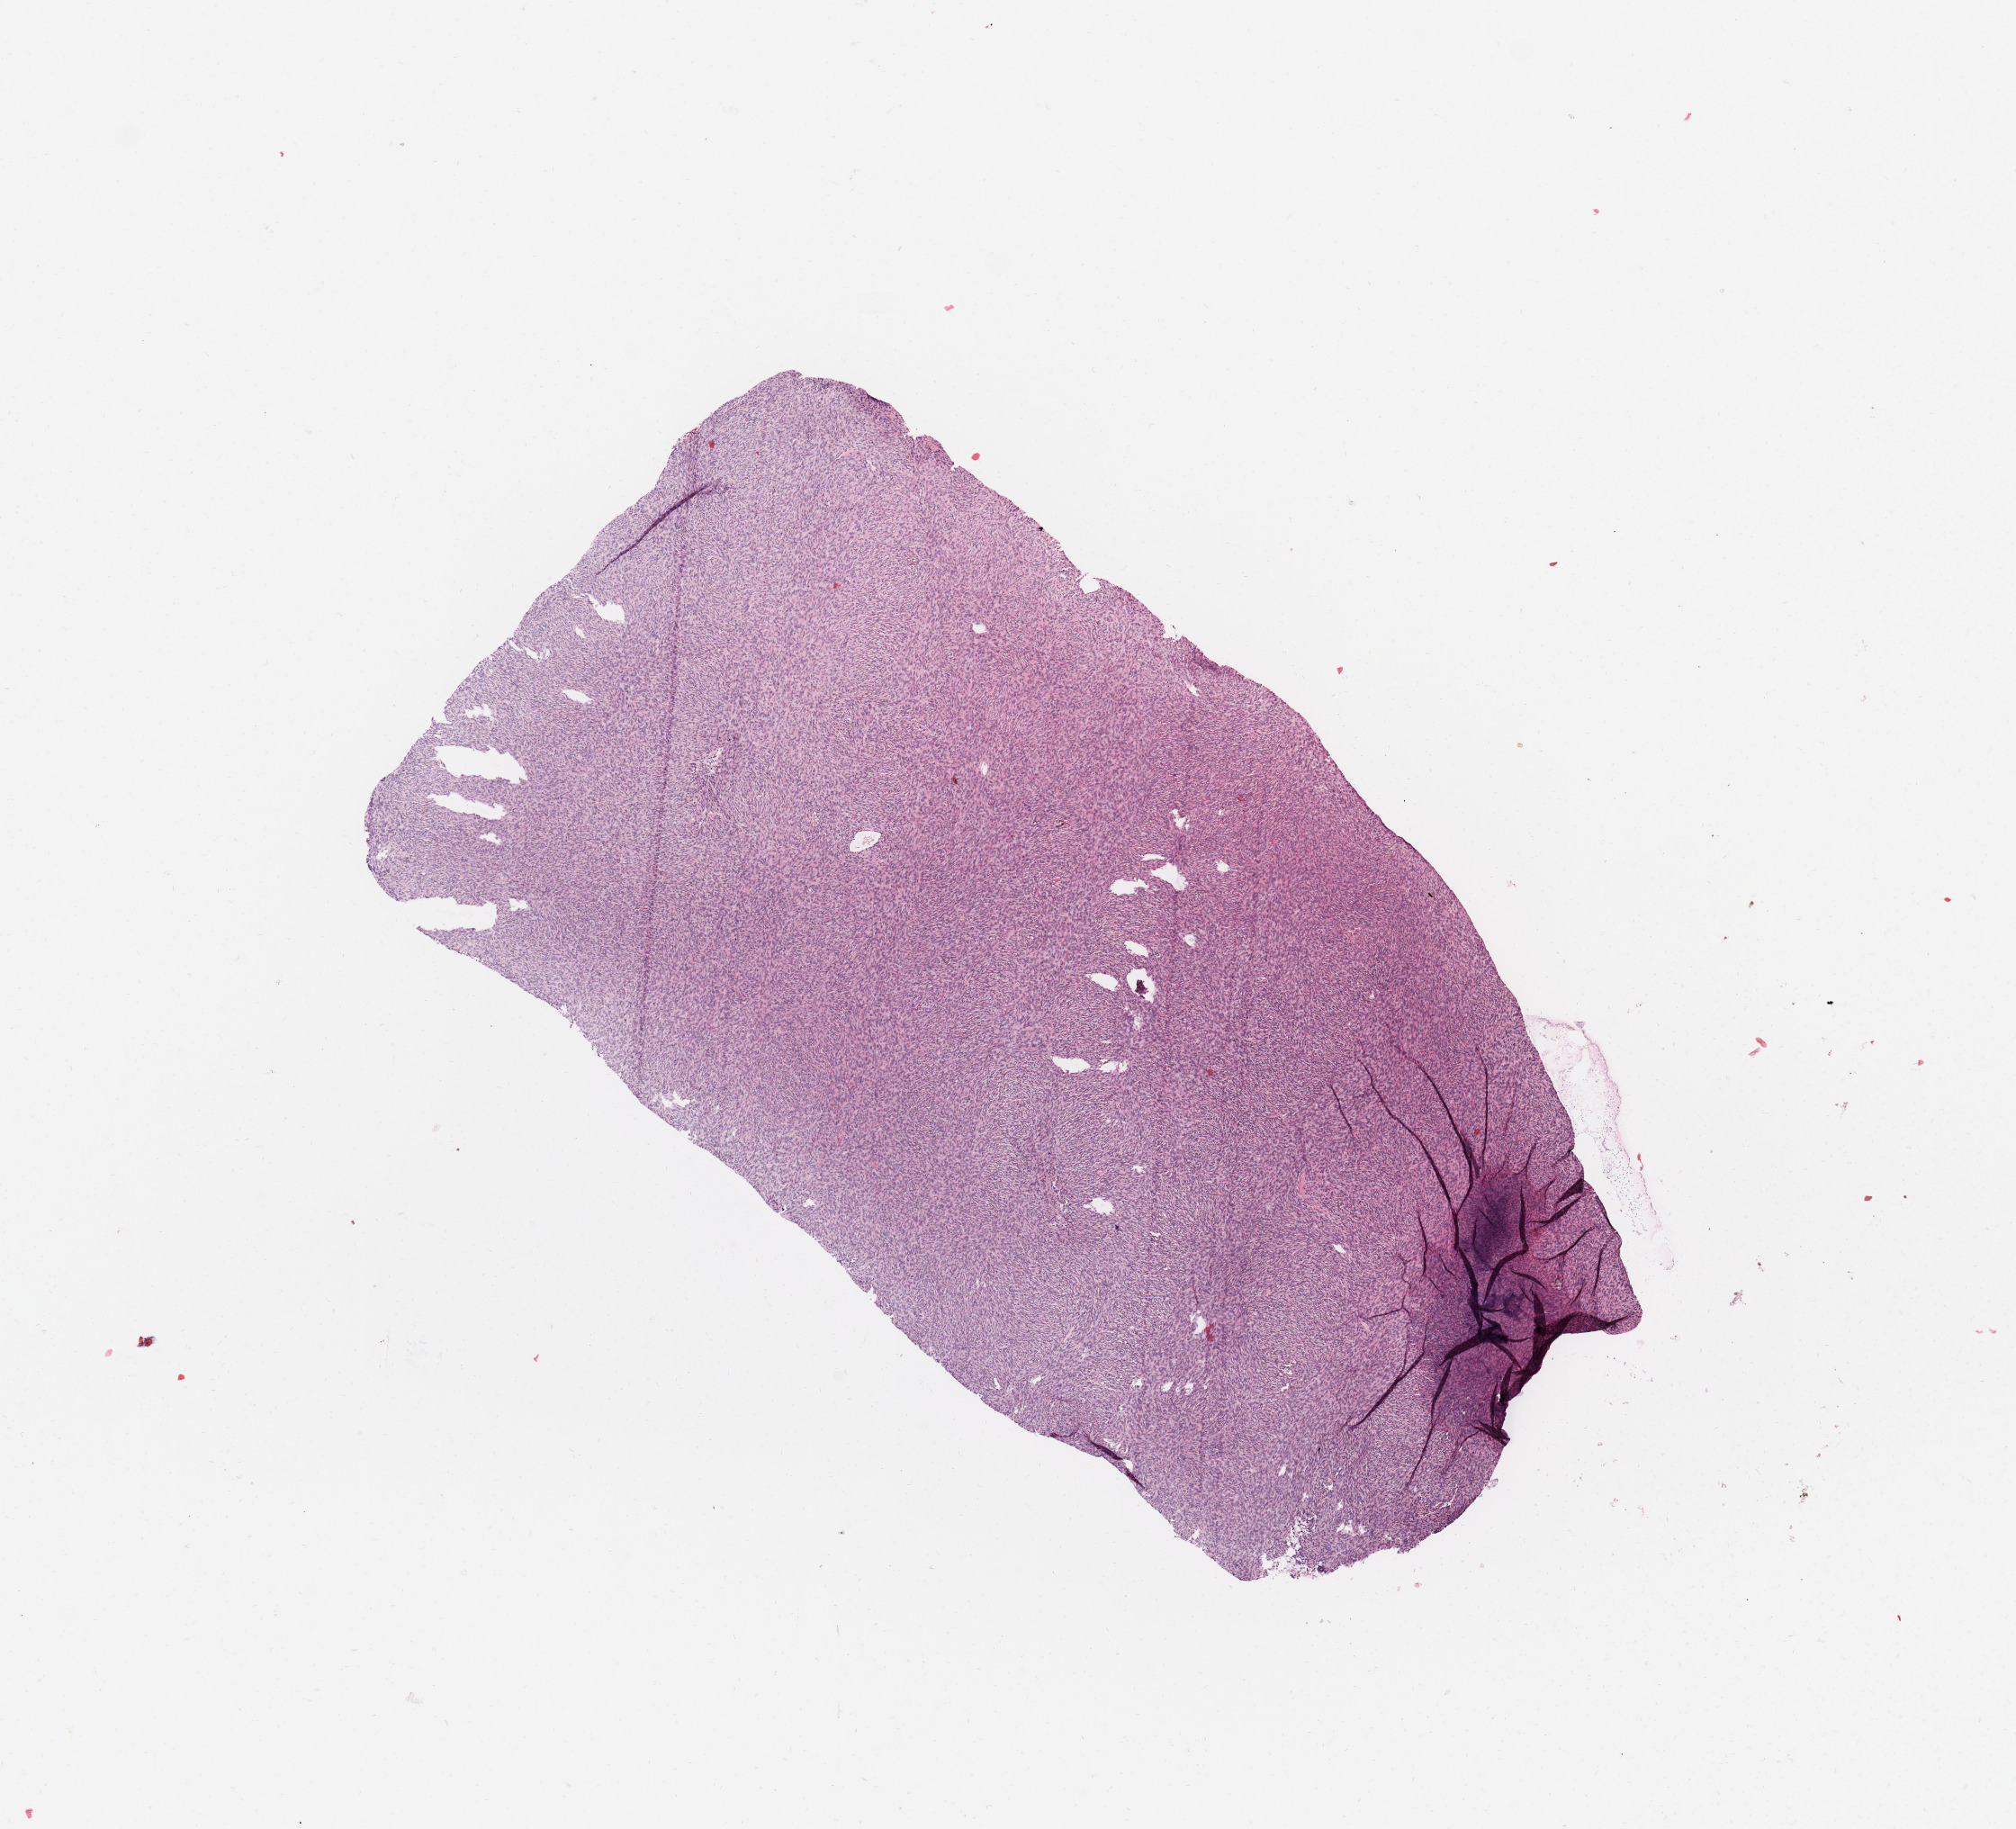
H&E-stained whole-slide image — low-resolution overview of the scanned area, about 8.9 x 8.0 mm (from a 20x scan), tumour tissue sample. Patient: male, age 42 years.
Patient diagnosis (cohort enrolment): sarcoma (site not recorded at cohort level).